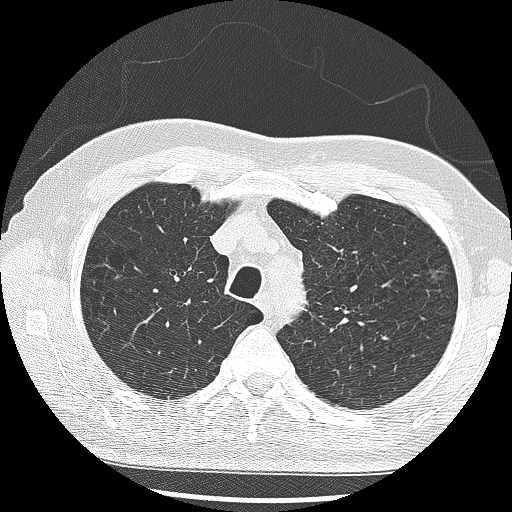
Low-dose screening chest CT, one axial slice. Position 220 of 285 along the scan axis. Reconstruction kernel LUNG. 120 kVp. Lung window (W 1500 / L -600 HU). 2.5 mm slice thickness. 512 × 512 image matrix, field of view 340 × 340 mm.
Annotated regions visible in this slice (expert manual segmentation):
- lesion 1 (tumor, upper lobe of left lung): bounding box (x1, y1, x2, y2) in pixels: (428, 269, 444, 283)